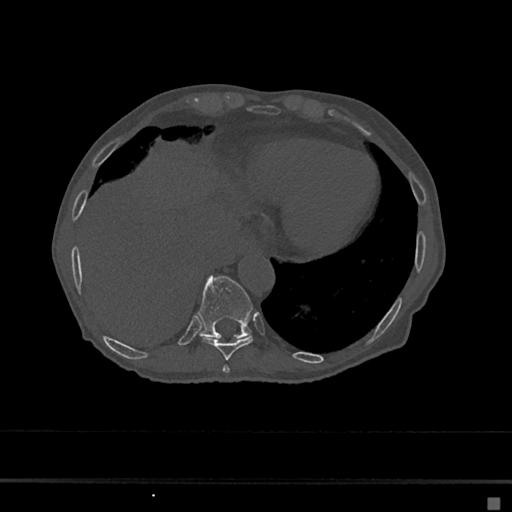
CT including the spine, one axial slice; slice 251 of 797 in the series (ordered by position); reconstruction kernel Br40s/3; bone window (W 1800 / L 400 HU); 0.5 mm slice thickness; 512 × 512 image matrix, field of view 360 × 360 mm. Patient: female, 68 years. Case-level facts recorded for this patient, not image findings: primary cancer: renal.
Annotated regions visible in this slice (semi-automatically segmented with operator editing):
- T10 vertebra: bounding box <197,276,253,339> (left, top, right, bottom; pixels)
- T8 vertebra: <223,365,230,374>
- T9 vertebra: <201,337,254,360>